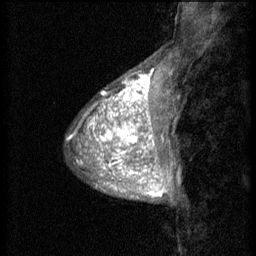
Breast MRI (dynamic contrast-enhanced), one sagittal slice. Slice 15 of 60 in the series (ordered by position). 3 images stored at this slice position (order not interpretable as contrast timing). 1.5 T. TE 4.2 ms, TR 8.2 ms. 256 × 256 image matrix, field of view 180 × 180 mm. Female patient, age 38 years.
Outlined on this slice (semi-automatically segmented with operator editing):
- analysis volume of interest (the breast-tissue region the enhancement analysis was run in; not a lesion): bounding box [x1, y1, x2, y2] px = [95, 106, 157, 171]
- tumour enhancement mask (voxels above the 70 % enhancement threshold inside the analysis volume of interest): [95, 106, 157, 171]